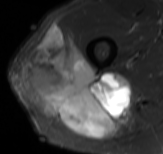
MRI of an extremity soft-tissue mass, one axial slice; slice 53 of 61 in the series (ordered by position); STIR; MR volume resampled by the dataset authors to the PET/CT grid (not the native acquisition matrix); 3.27 mm slice thickness; 163 × 154 image matrix. Male patient. From the clinical record (not read from this slice): histological type: poorly differentiated synovial sarcoma; grade: high; site of the primary tumour: right buttock.
Outlined on this slice (expert contour drawn on MRI and transferred to this co-registered scan by the dataset authors):
- gross tumour volume including surrounding oedema: box from (x=21, y=25) to (x=131, y=140) px
- gross tumour volume (mass): (x=21, y=25)–(x=129, y=140)